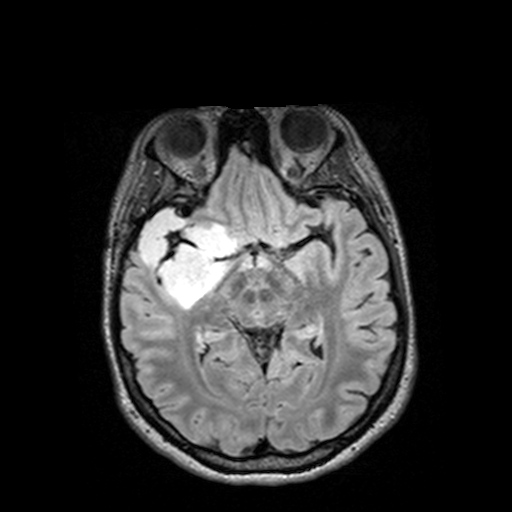
Brain MRI from a brain-tumour surgery series, one axial slice. T2 FLAIR. 512 × 512 image matrix. From the clinical record (not read from this slice): histopathology: Astrocytoma; WHO grade: 3; IDH mutation: yes; tumour location: Right Insular Temporal.
Outlined on this slice (manually delineated by an expert):
- tumour: box from (x=126, y=211) to (x=232, y=307) px